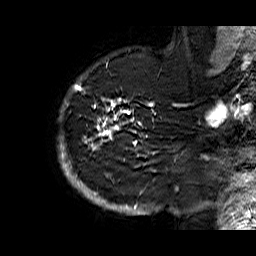
Breast MRI (dynamic contrast-enhanced), one sagittal slice; slice 51 of 60 in the series (ordered by position); dynamic contrast-enhanced series, time point 2 of 6 at this slice position (early post-contrast); 1.5 T; TE 6.3 ms, TR 32.9 ms; 4 mm slice thickness; 256 × 256 image matrix, field of view 200 × 200 mm. Female patient. Case-level facts recorded for this patient, not image findings: setting: breast cancer imaged before/during neoadjuvant chemotherapy; receptor status: HR-positive, HER2-negative.
Annotated regions visible in this slice (semi-automatically segmented with operator editing):
- analysis volume of interest (the breast-tissue region the enhancement analysis was run in; not a lesion): bounding box <58,74,176,210> (left, top, right, bottom; pixels)
- tumour enhancement mask (voxels above the 100 % enhancement threshold inside the analysis volume of interest): <58,77,175,210>